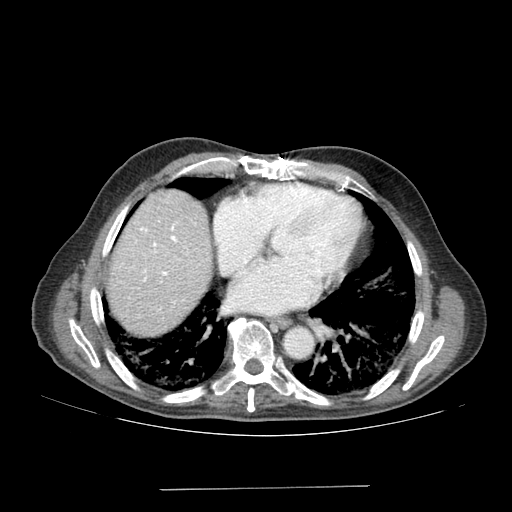
Contrast-enhanced abdominal CT (liver protocol), one axial slice; slice 170 of 192 in the series (ordered by position); soft-tissue window (W 400 / L 40 HU); 2.5 mm slice thickness; 512 × 512 image matrix, field of view 400 × 400 mm. Case-level facts recorded for this patient, not image findings: diagnosis: hepatocellular carcinoma (patient treated with transarterial chemoembolisation; whether this scan precedes or follows treatment is not stated here); TNM stage (as recorded): Stage-IVA; Child-Pugh class: A.
Outlined on this slice (semi-automatic segmentation, software-assisted and operator-edited):
- liver parenchyma outside the tumour (the mass and vessels are separate outlines, so this box may not span the whole liver): bounding box <106,190,212,336> (left, top, right, bottom; pixels)
- liver vessels: <141,226,177,281>